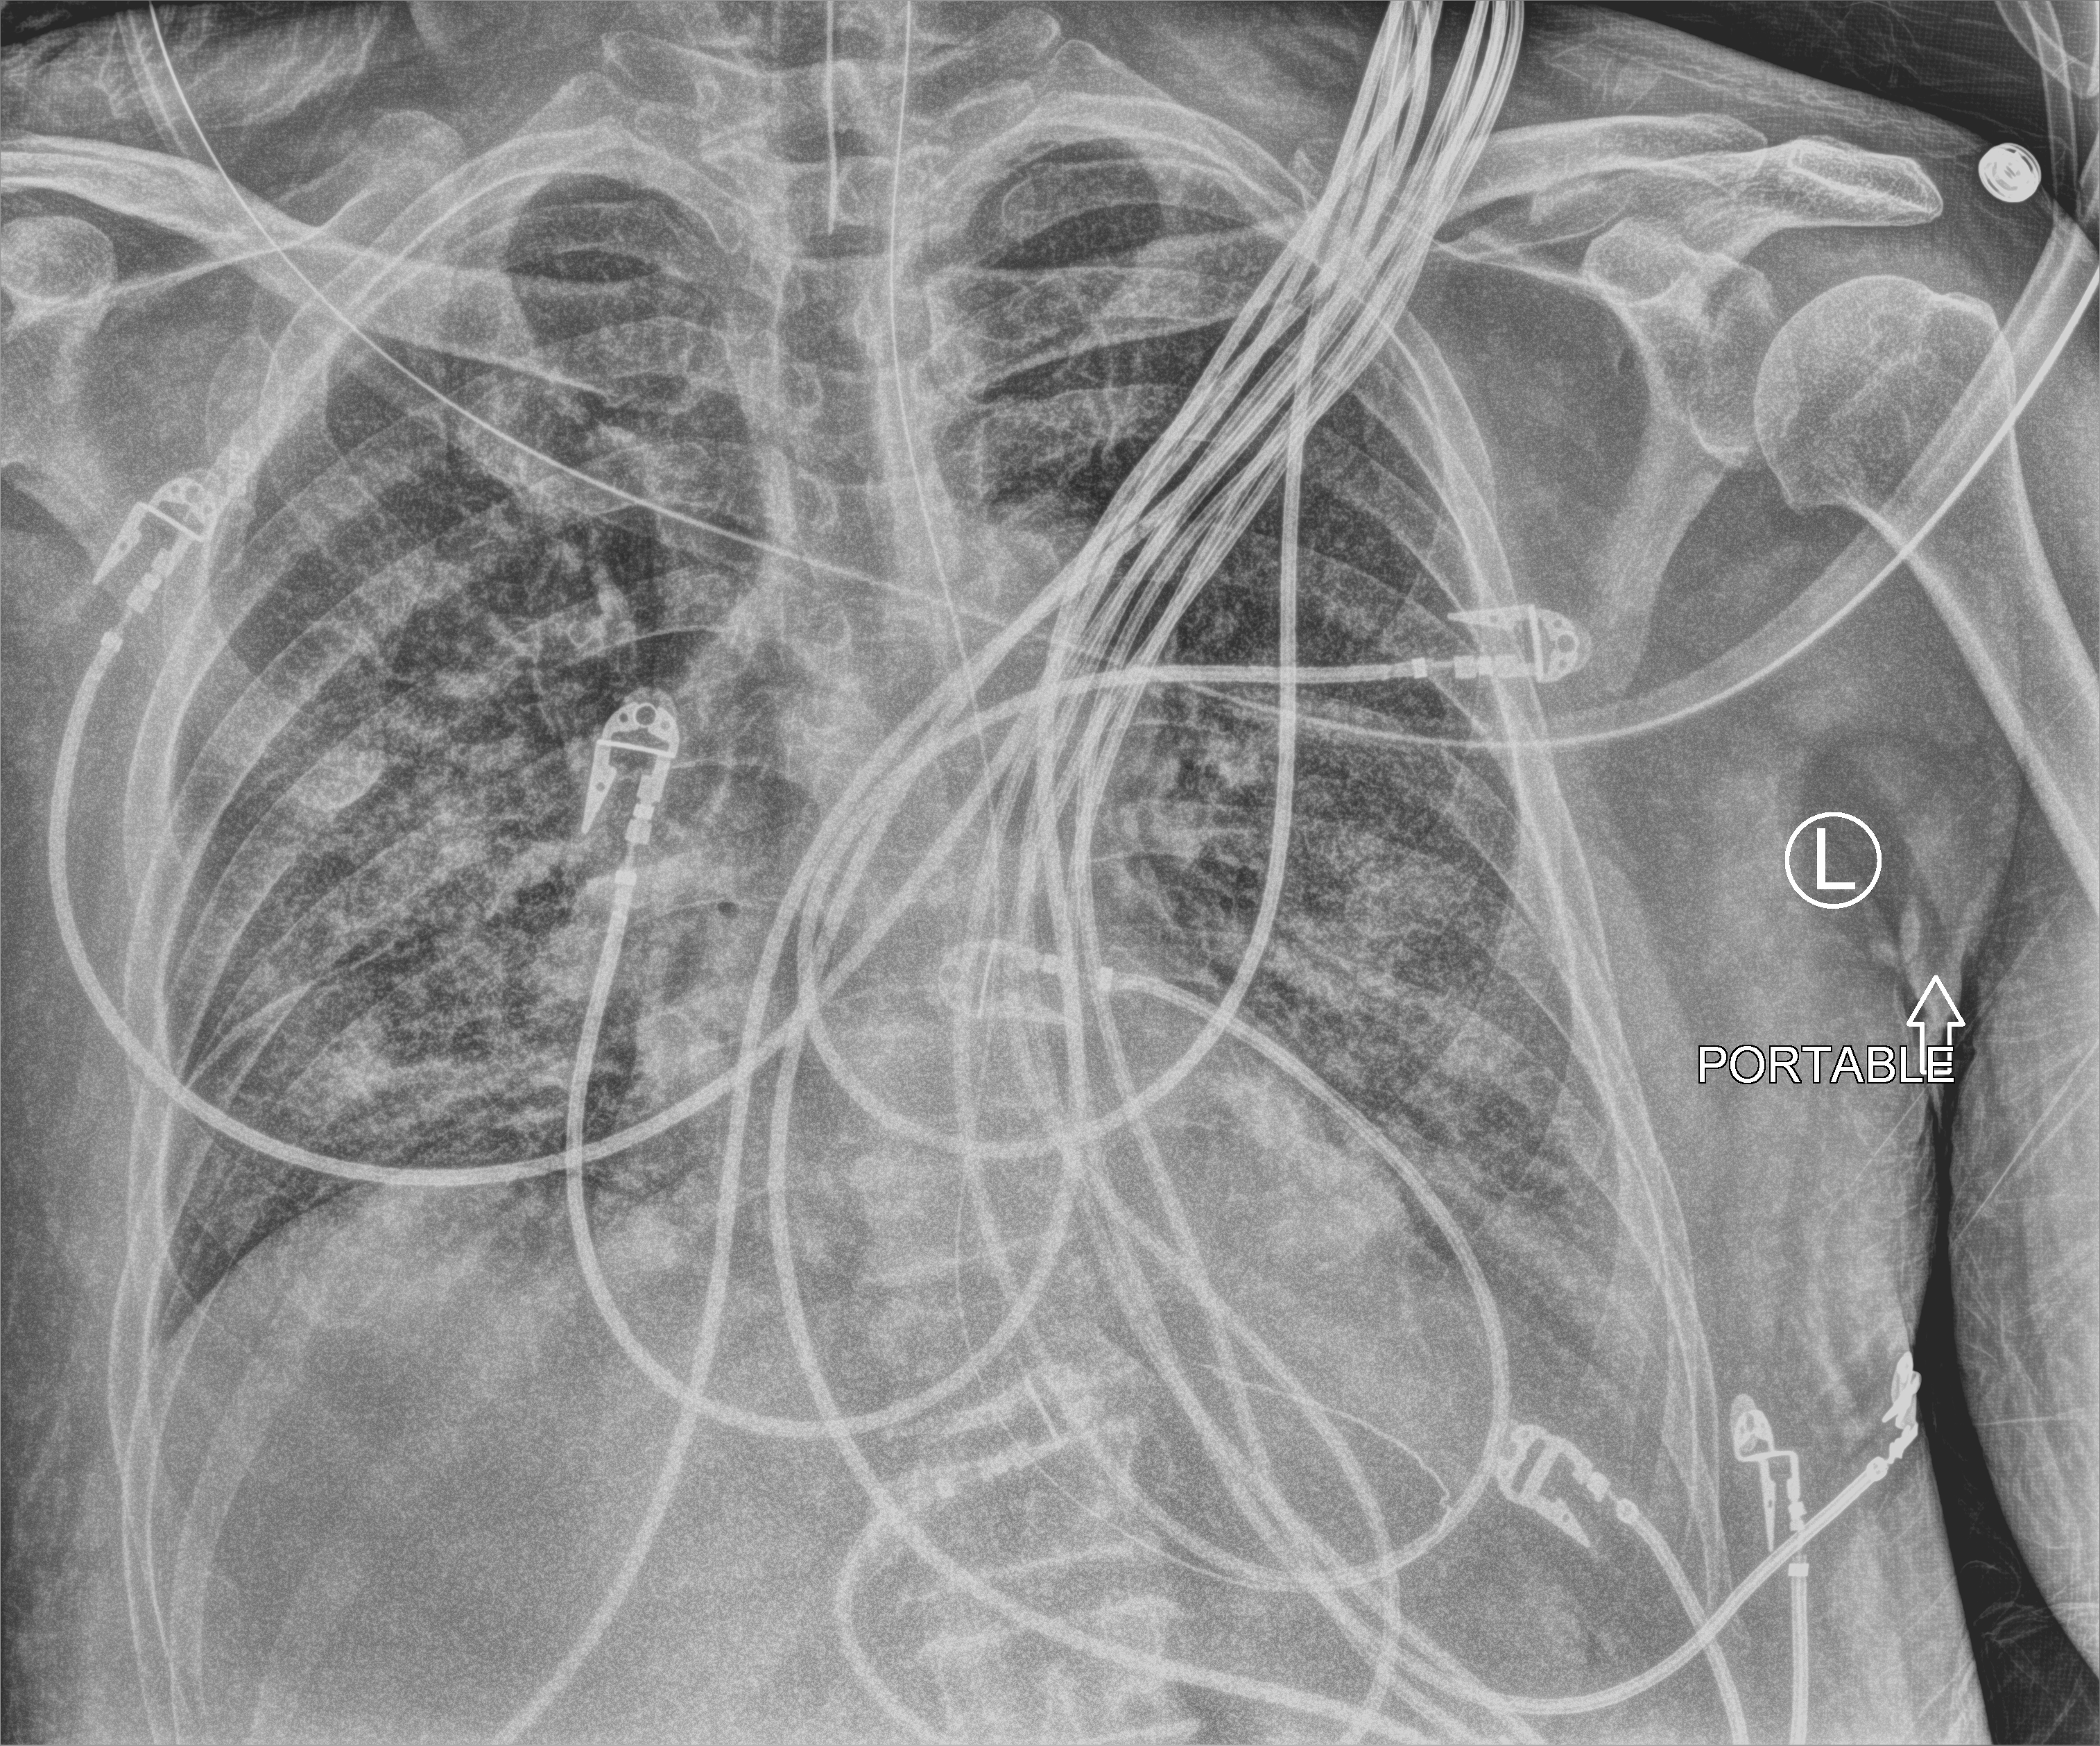
Portable chest radiograph, anteroposterior (AP) projection. Male patient hospitalised with COVID-19, age 60–74 years.
From the hospital-stay record, not from the radiograph (when in the stay this image was taken is not recorded):
- admitted to intensive care during this hospital stay: yes
- diabetes (admission record): yes